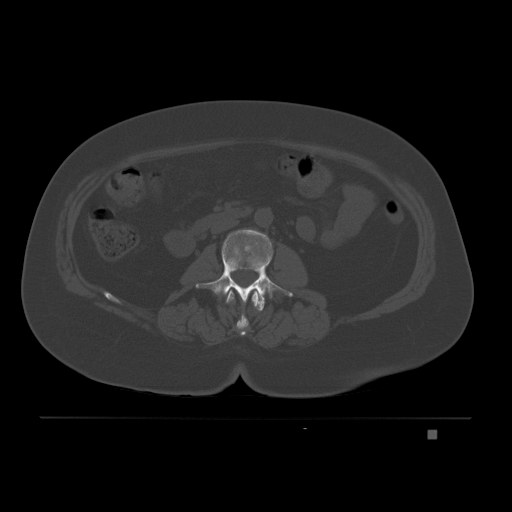
CT including the spine, one axial slice. Slice 61 of 221 in the series (ordered by position). Bone window (W 1800 / L 400 HU). 3 mm slice thickness. 512 × 512 image matrix. Female patient, age 63 years. Case-level facts recorded for this patient, not image findings: primary cancer: breast.
Structures marked on this image (semi-automatically segmented with operator editing):
- L1 vertebra: bounding box (x1, y1, x2, y2) in pixels: (225, 290, 261, 336)
- L2 vertebra: (196, 229, 293, 312)